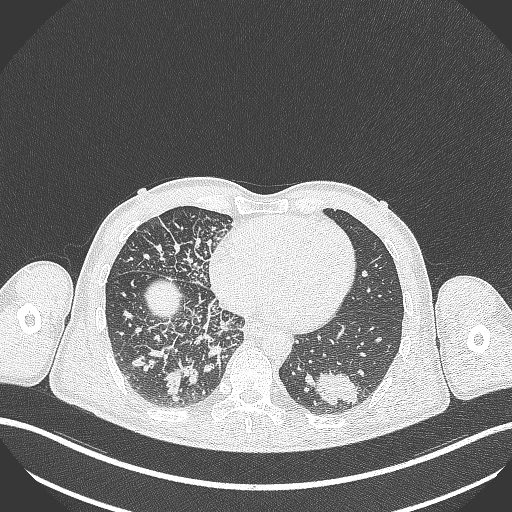
Chest CT, one axial slice; slice 102 of 348 in the series (ordered by position); reconstruction kernel B70f; 120 kVp; lung window (W 1500 / L -600 HU); 1 mm slice thickness; 512 × 512 image matrix, field of view 400 × 400 mm. Male patient, age 49 years. Case-level facts recorded for this patient, not image findings: clinical TNM (as recorded): T2b N1 M0.
Structures marked on this image (bounding box drawn by a radiologist):
- lung tumour (recorded histology: adenocarcinoma): box from (x=316, y=364) to (x=363, y=407) px